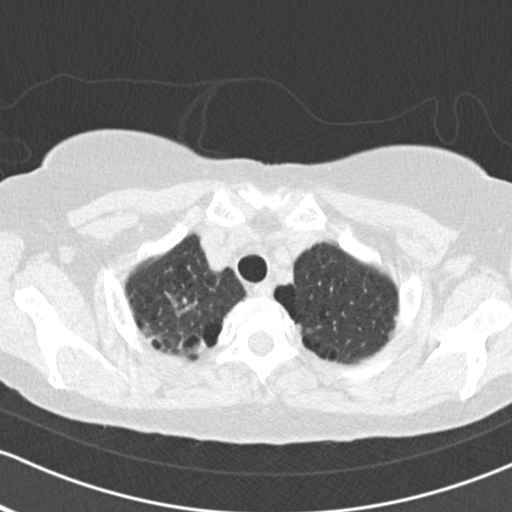
Chest CT (low-dose screening protocol), one axial image, second annual screen, lung window (W 1500 / L -600 HU), 2 mm slice thickness. Female participant, aged 64 years at enrolment. Current smoker at enrolment.
• Lesion marked by an expert reader, bounding box (x1, y1, x2, y2) in pixels: (172, 325, 219, 368).
• Screening reader's record for this exam (one nodule recorded; not confirmed to be the boxed lesion): non-calcified nodule or mass ≥4 mm, right upper lobe, 16 × 15 mm, spiculated (stellate) margins, soft tissue attenuation, pre-existing on the prior screen: no.
• Official screen result: positive, other.
• Lung cancer was diagnosed 45 days after this screen: adenocarcinoma, NOS, right upper lobe, poorly differentiated (G3), stage IB (AJCC 6th edition), 15 mm at pathology.